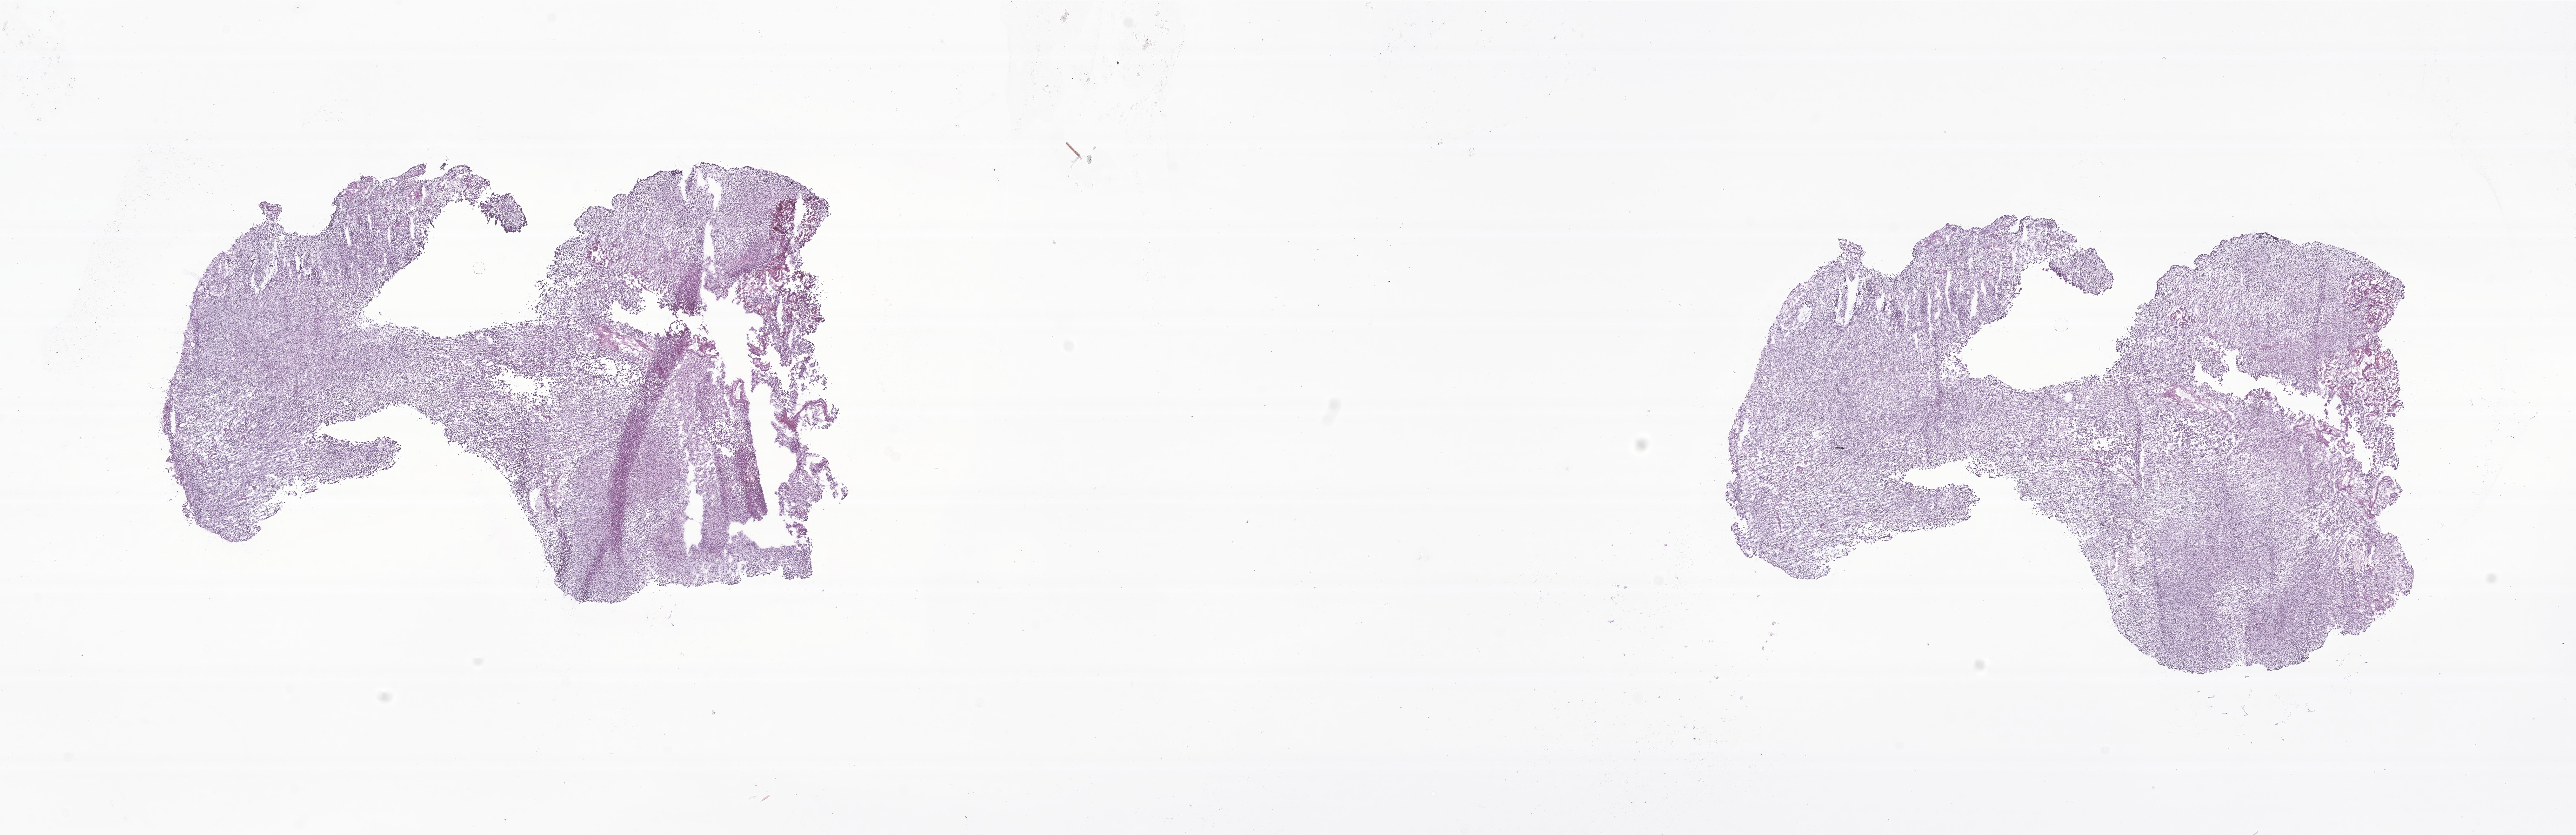
Whole-slide image, hematoxylin and eosin (H&E) stain of tumor tissue from the cerebellum — whole scanned area (about 31.0 x 10.0 mm) shown as a low-resolution overview; frozen section (OCT-embedded). Patient male; age 137 months (11 years 5 months).
- diagnosis: Medulloblastoma, NOS